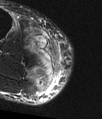
MRI of an extremity soft-tissue mass, one axial slice. Position 36 of 48 along the scan axis. T2-weighted fat-saturated. MR volume resampled by the dataset authors to the PET/CT grid (not the native acquisition matrix). 3.27 mm slice thickness. 102 × 119 image matrix. Male patient. Case-level facts recorded for this patient, not image findings: histological type: pleiomorphic liposarcoma; grade: high; site of the primary tumour: right calf.
Outlined on this slice (expert contour drawn on MRI and transferred to this co-registered scan by the dataset authors):
- gross tumour volume including surrounding oedema: bounding box (x1, y1, x2, y2) in pixels: (42, 37, 59, 75)